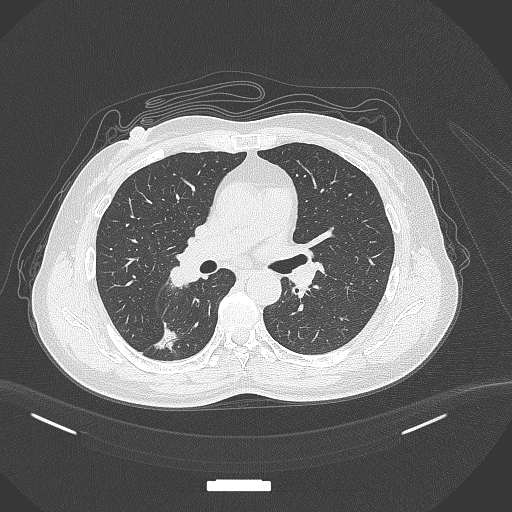
Chest CT, one axial slice; slice 174 of 352 in the series (ordered by position); reconstruction kernel B70f; lung window (W 1500 / L -600 HU); 1 mm slice thickness; 512 × 512 image matrix. Female patient, age 55 years. From the clinical record (not read from this slice): clinical TNM (as recorded): T1c N1 M0.
Structures marked on this image (bounding box drawn by a radiologist):
- lung tumour (recorded histology: adenocarcinoma): bounding box [x1, y1, x2, y2] px = [152, 320, 182, 358]